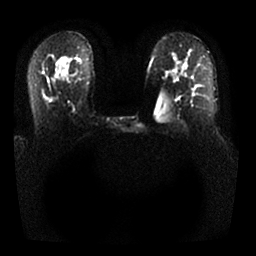
Breast MRI, one axial slice; slice 18 of 25 in the series (ordered by position); diffusion-weighted series; image 2 of 4 stored at this slice position (different b-values; order by instance number); 1.5 T; 4 mm slice thickness; 256 × 256 image matrix, field of view 350 × 350 mm. Female patient.
Structures marked on this image (outlined manually by an expert reader):
- tumour on diffusion-weighted imaging: box from (x=44, y=95) to (x=49, y=101) px